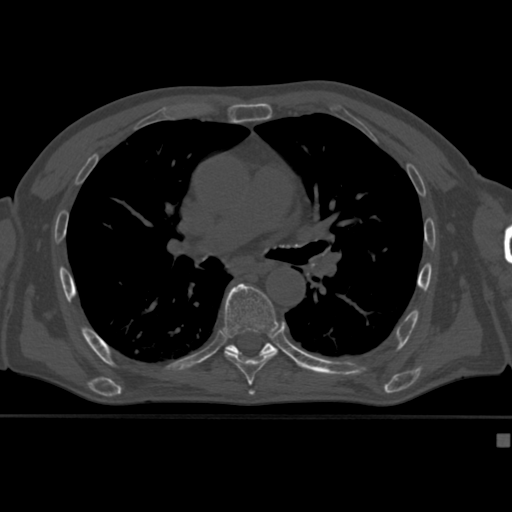
CT including the spine, one axial slice. Slice 275 of 430 in the series (ordered by position). Reconstruction kernel Br40s. 120 kVp. Bone window (W 1800 / L 400 HU). 1.5 mm slice thickness. 512 × 512 image matrix. Male patient, age 64 years. Case-level facts recorded for this patient, not image findings: primary cancer: uterus.
Annotated regions visible in this slice (semi-automatic segmentation, software-assisted and operator-edited):
- T7 vertebra: bounding box [x1, y1, x2, y2] px = [223, 283, 279, 382]
- T8 vertebra: [224, 343, 277, 357]